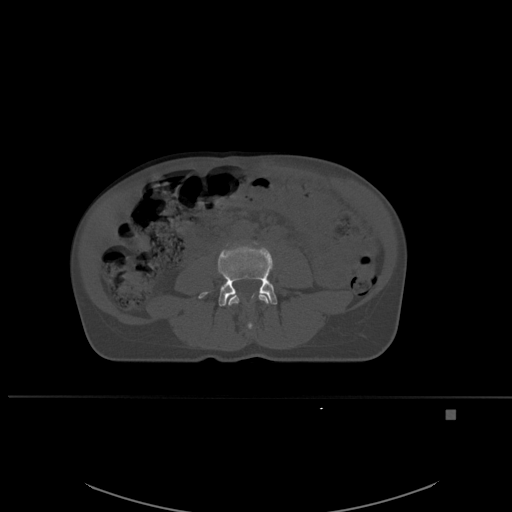
CT including the spine, one axial slice. Position 199 of 537 along the scan axis. Bone window (W 1800 / L 400 HU). 512 × 512 image matrix, field of view 440 × 440 mm. Female patient, age 45 years. From the clinical record (not read from this slice): primary cancer: lung.
Annotated regions visible in this slice (semi-automatic segmentation, software-assisted and operator-edited):
- L3 vertebra: bounding box <228,293,270,329> (left, top, right, bottom; pixels)
- L4 vertebra: <198,242,278,307>